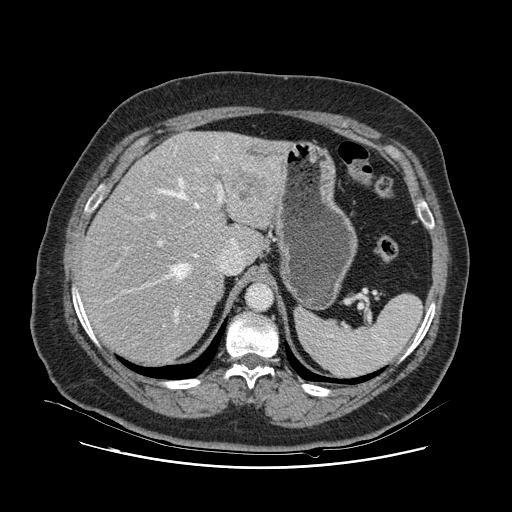
Contrast-enhanced abdominal CT, one axial slice; slice 83 of 132 in the series (ordered by position); intravenous contrast given; soft-tissue window (W 400 / L 40 HU); 2.5 mm slice thickness; 512 × 512 image matrix, field of view 391 × 391 mm. Female patient, age 73 years. From the clinical record (not read from this slice): diagnosis: colorectal cancer liver metastases, imaged before liver resection; multiple liver metastases: no; largest metastasis: 7 cm; disease in both lobes: no.
Outlined on this slice (expert manual segmentation):
- hepatic veins: box from (x=122, y=155) to (x=234, y=323) px
- liver: (x=83, y=132)–(x=284, y=364)
- planned liver remnant (the part of the liver to remain after resection): (x=83, y=160)–(x=239, y=364)
- portal vein (with intrahepatic branches): (x=125, y=169)–(x=224, y=327)
- liver metastasis: (x=232, y=170)–(x=270, y=202)